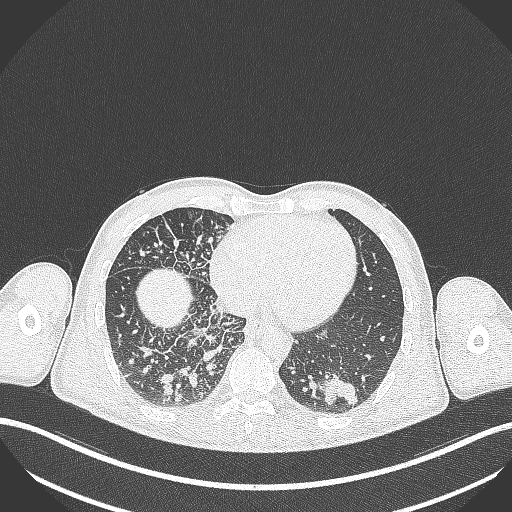
Chest CT, one axial slice; position 97 of 348 along the scan axis; reconstruction kernel B70f; lung window (W 1500 / L -600 HU); 512 × 512 image matrix, field of view 400 × 400 mm. Male patient, age 49 years. Case-level facts recorded for this patient, not image findings: clinical TNM (as recorded): T2b N1 M0.
Annotated regions visible in this slice (rectangle marked by the reading radiologist):
- lung tumour (recorded histology: adenocarcinoma): bounding box [x1, y1, x2, y2] px = [315, 368, 366, 410]